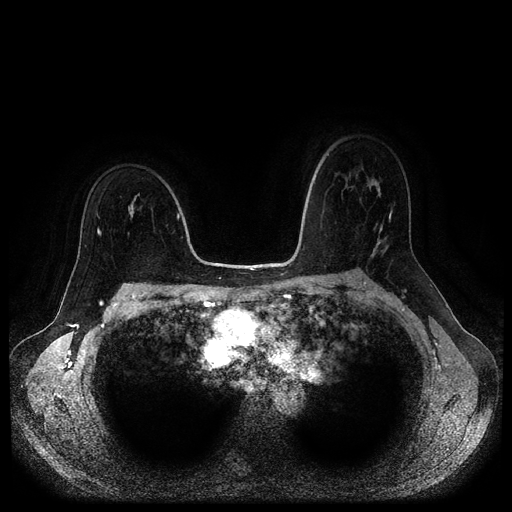
Breast MRI (dynamic contrast-enhanced, multi-phase), one axial slice; dynamic contrast-enhanced series, time point 2 of 5 at this slice position (early post-contrast); 1.5 T; TE 2.6 ms, TR 5.3 ms; 2 mm slice thickness; 512 × 512 image matrix. Female patient, age 50 years.
Annotated regions visible in this slice (semi-automatic segmentation, software-assisted and operator-edited):
- breast lesion (labelled benign in the annotation): bounding box <128,195,137,221> (left, top, right, bottom; pixels)